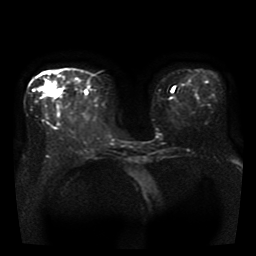
Breast MRI, one axial slice. Slice 14 of 41 in the series (ordered by position). Diffusion-weighted series; image 2 of 4 stored at this slice position (different b-values; order by instance number). 1.5 T. 256 × 256 image matrix, field of view 330 × 330 mm. Female patient.
Outlined on this slice (manually delineated by an expert):
- tumour on diffusion-weighted imaging: box from (x=47, y=81) to (x=62, y=97) px